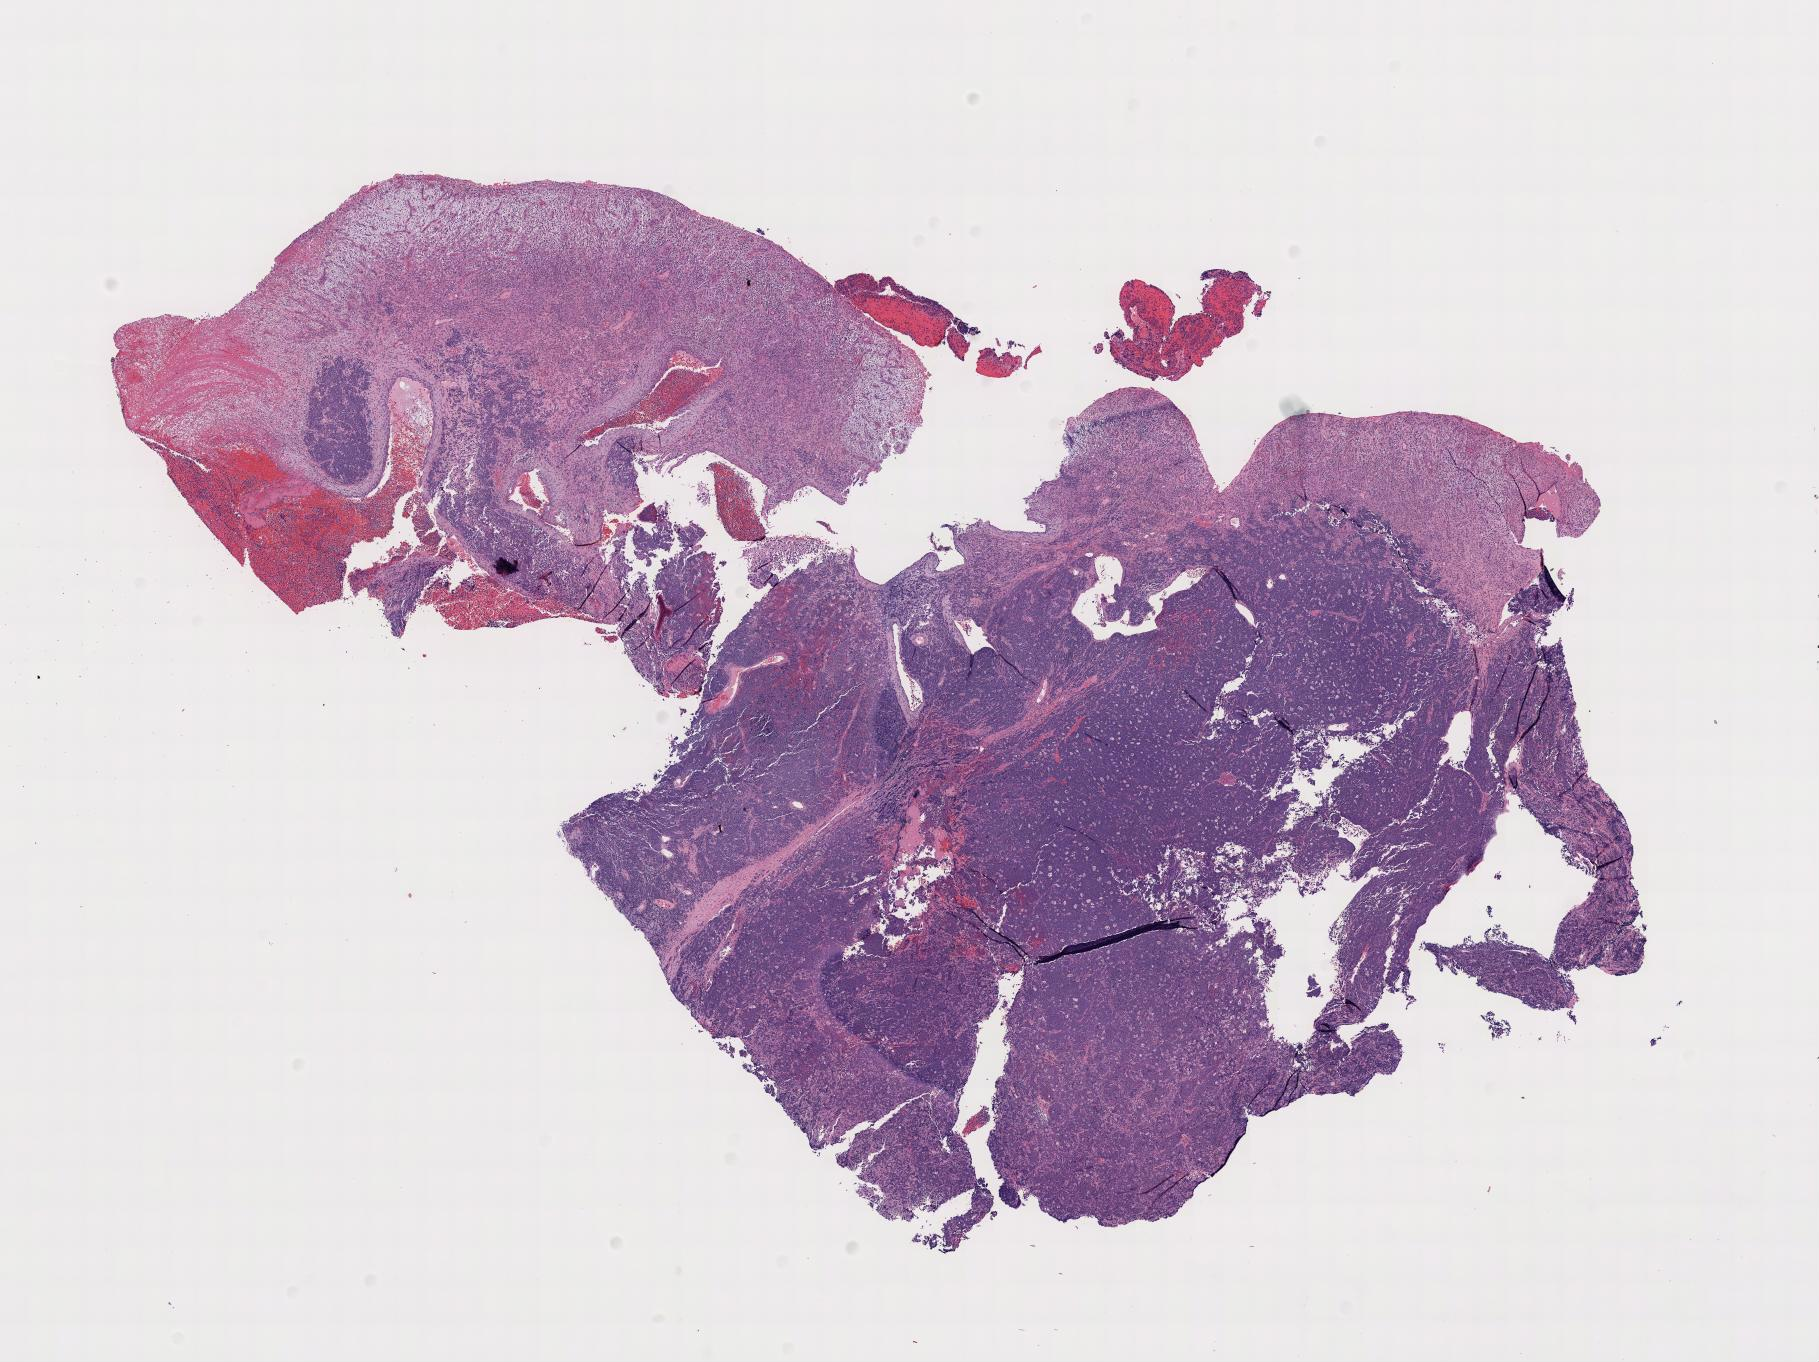
Digitized hematoxylin and eosin (H&E)-stained section — a low-resolution overview of the entire scanned area. Specimen: tumor tissue. Site: mandible. Patient: male, age at initial diagnosis 6 years.
• histologic diagnosis: Burkitt lymphoma, NOS